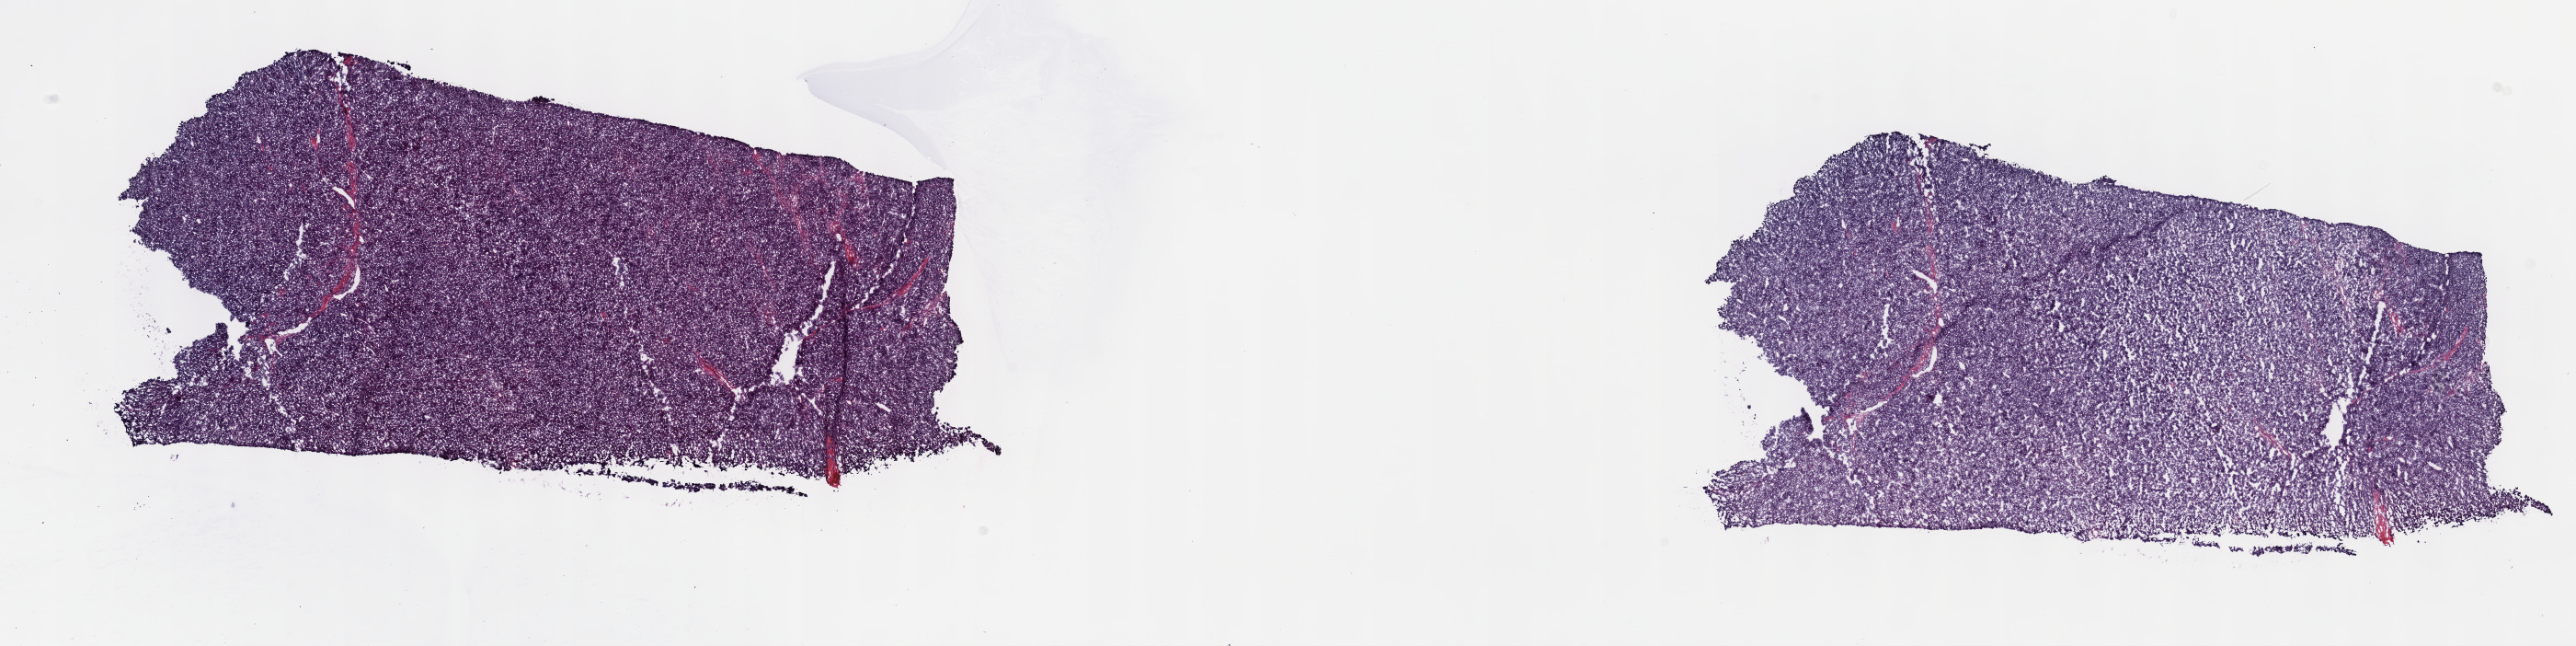
Hematoxylin and eosin (H&E) stained whole-slide image — a low-resolution overview of the entire scanned area, about 22.7 x 5.7 mm (acquisition: 40x scan); frozen section from the top of the tissue portion; primary tumour sample from the thymus. Patient: male, age at initial diagnosis 52 years. Pathologist review of this section (percent, as recorded): tumour cells 100%, tumour nuclei 80%, normal cells 0%, stromal cells 0%, necrosis 0%. Inflammatory infiltration, as recorded: lymphocyte infiltration 2%, monocyte infiltration 0%, neutrophil infiltration 0%.
Diagnosis: Thymoma, type B2, NOS.